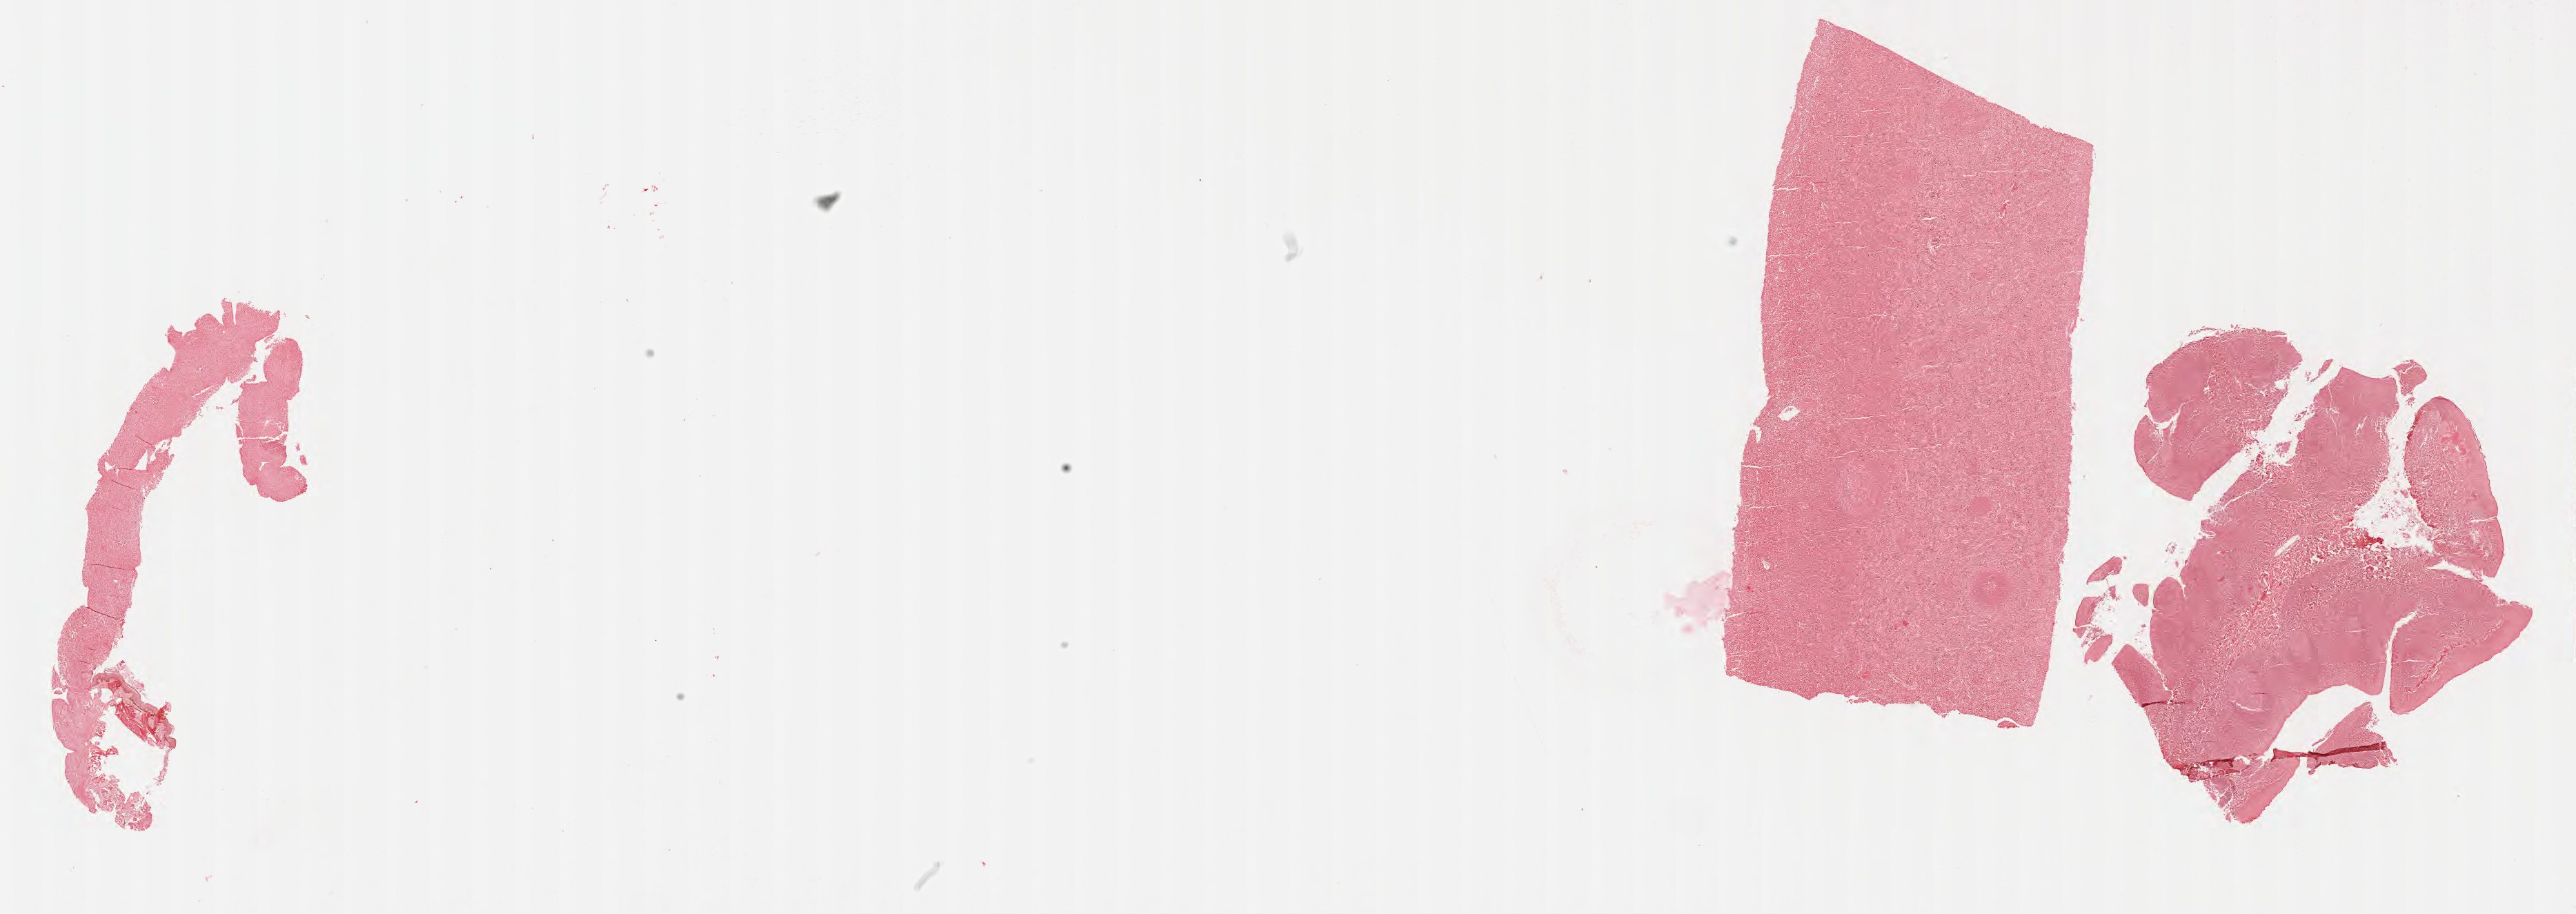
In-situ hybridisation whole-slide image, Epstein–Barr virus-encoded RNA (EBER) probe, a low-resolution overview of the entire scanned area, about 30.2 x 10.7 mm. Specimen: tumor tissue. Female patient, age 43 years.
Histologic diagnosis: Diffuse large B-cell lymphoma, NOS.